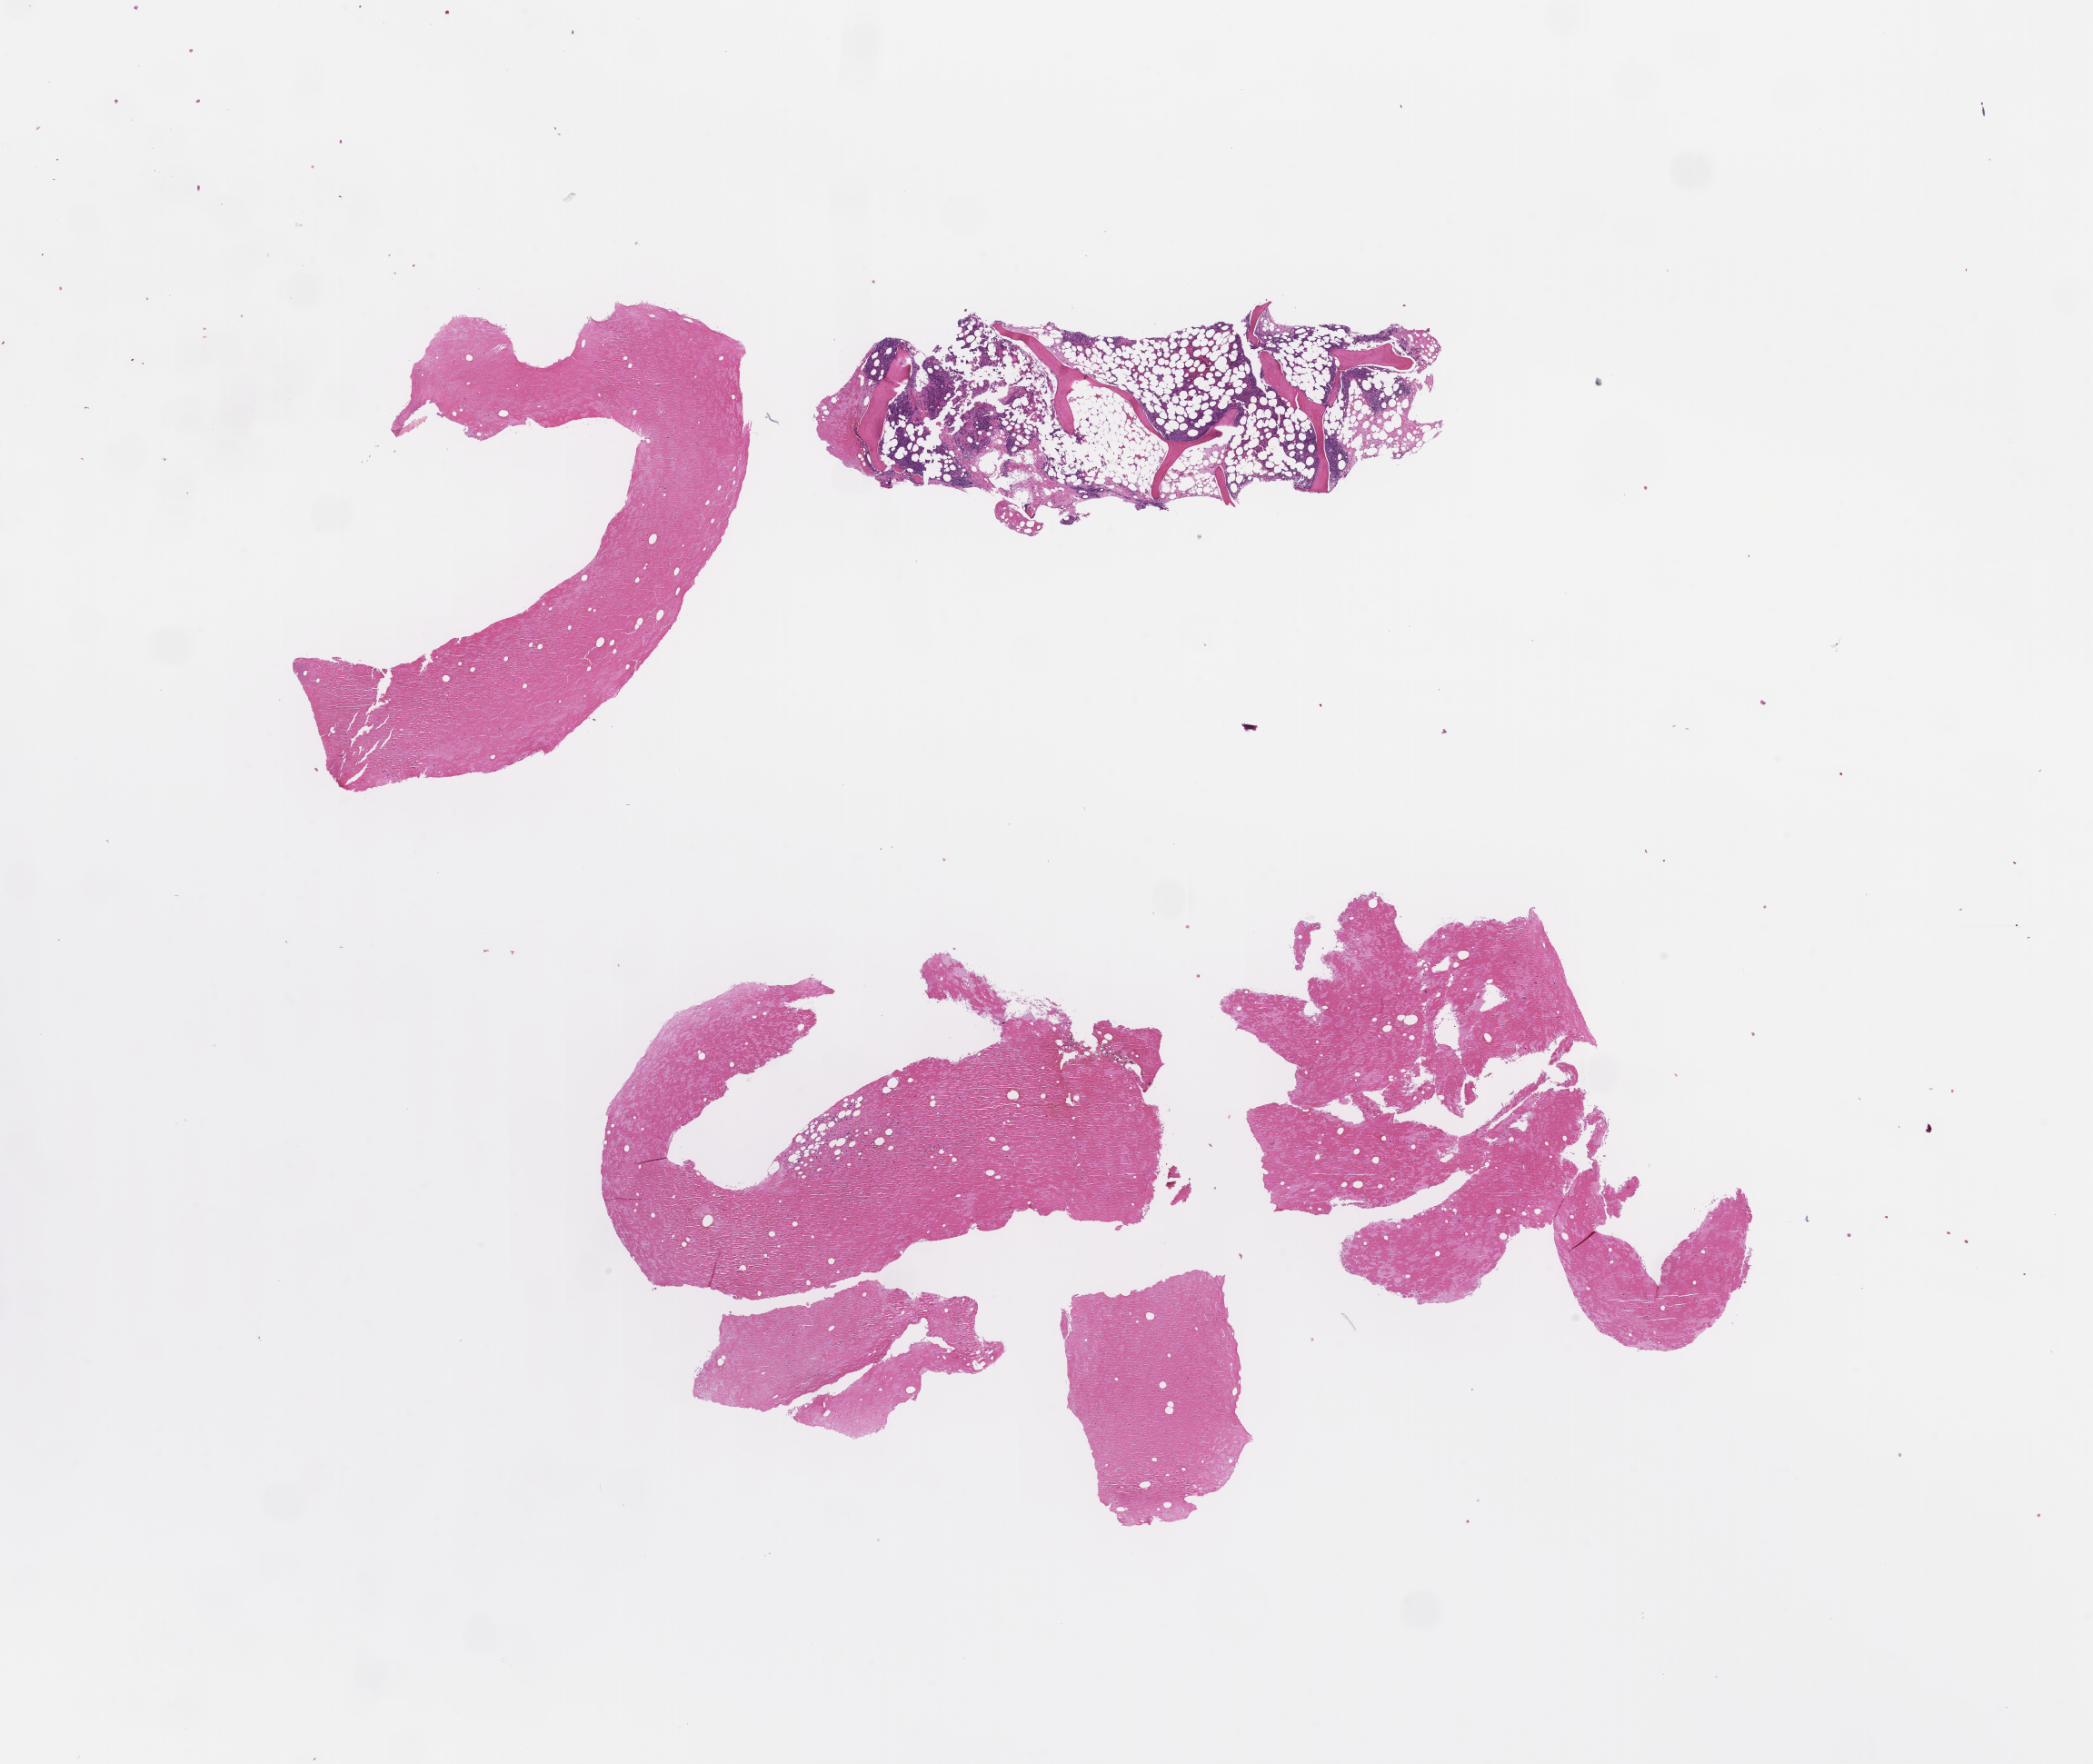
Whole-slide image, H&E stain — a low-resolution overview of the entire scanned area, about 18.6 x 15.7 mm, formalin-fixed, paraffin-embedded (FFPE) tissue, site: bone marrow, specimen time point: archival tissue. Patient sex: female.
This section: primary tumor. Diagnosis: Plasma Cell Myeloma.